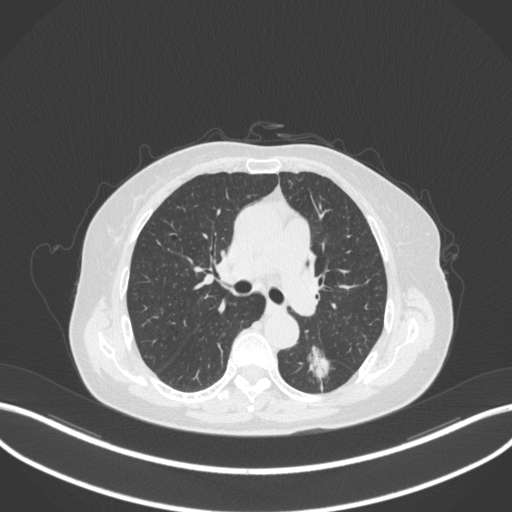
Chest CT, one axial slice. Slice 182 of 352 in the series (ordered by position). 120 kVp. Lung window (W 1500 / L -600 HU). 512 × 512 image matrix, field of view 400 × 400 mm. Patient: female, 70 years. From the clinical record (not read from this slice): clinical TNM (as recorded): T1c N0 M0.
Structures marked on this image (bounding box drawn by a radiologist):
- lung tumour (recorded histology: adenocarcinoma): bounding box [x1, y1, x2, y2] px = [305, 341, 335, 383]